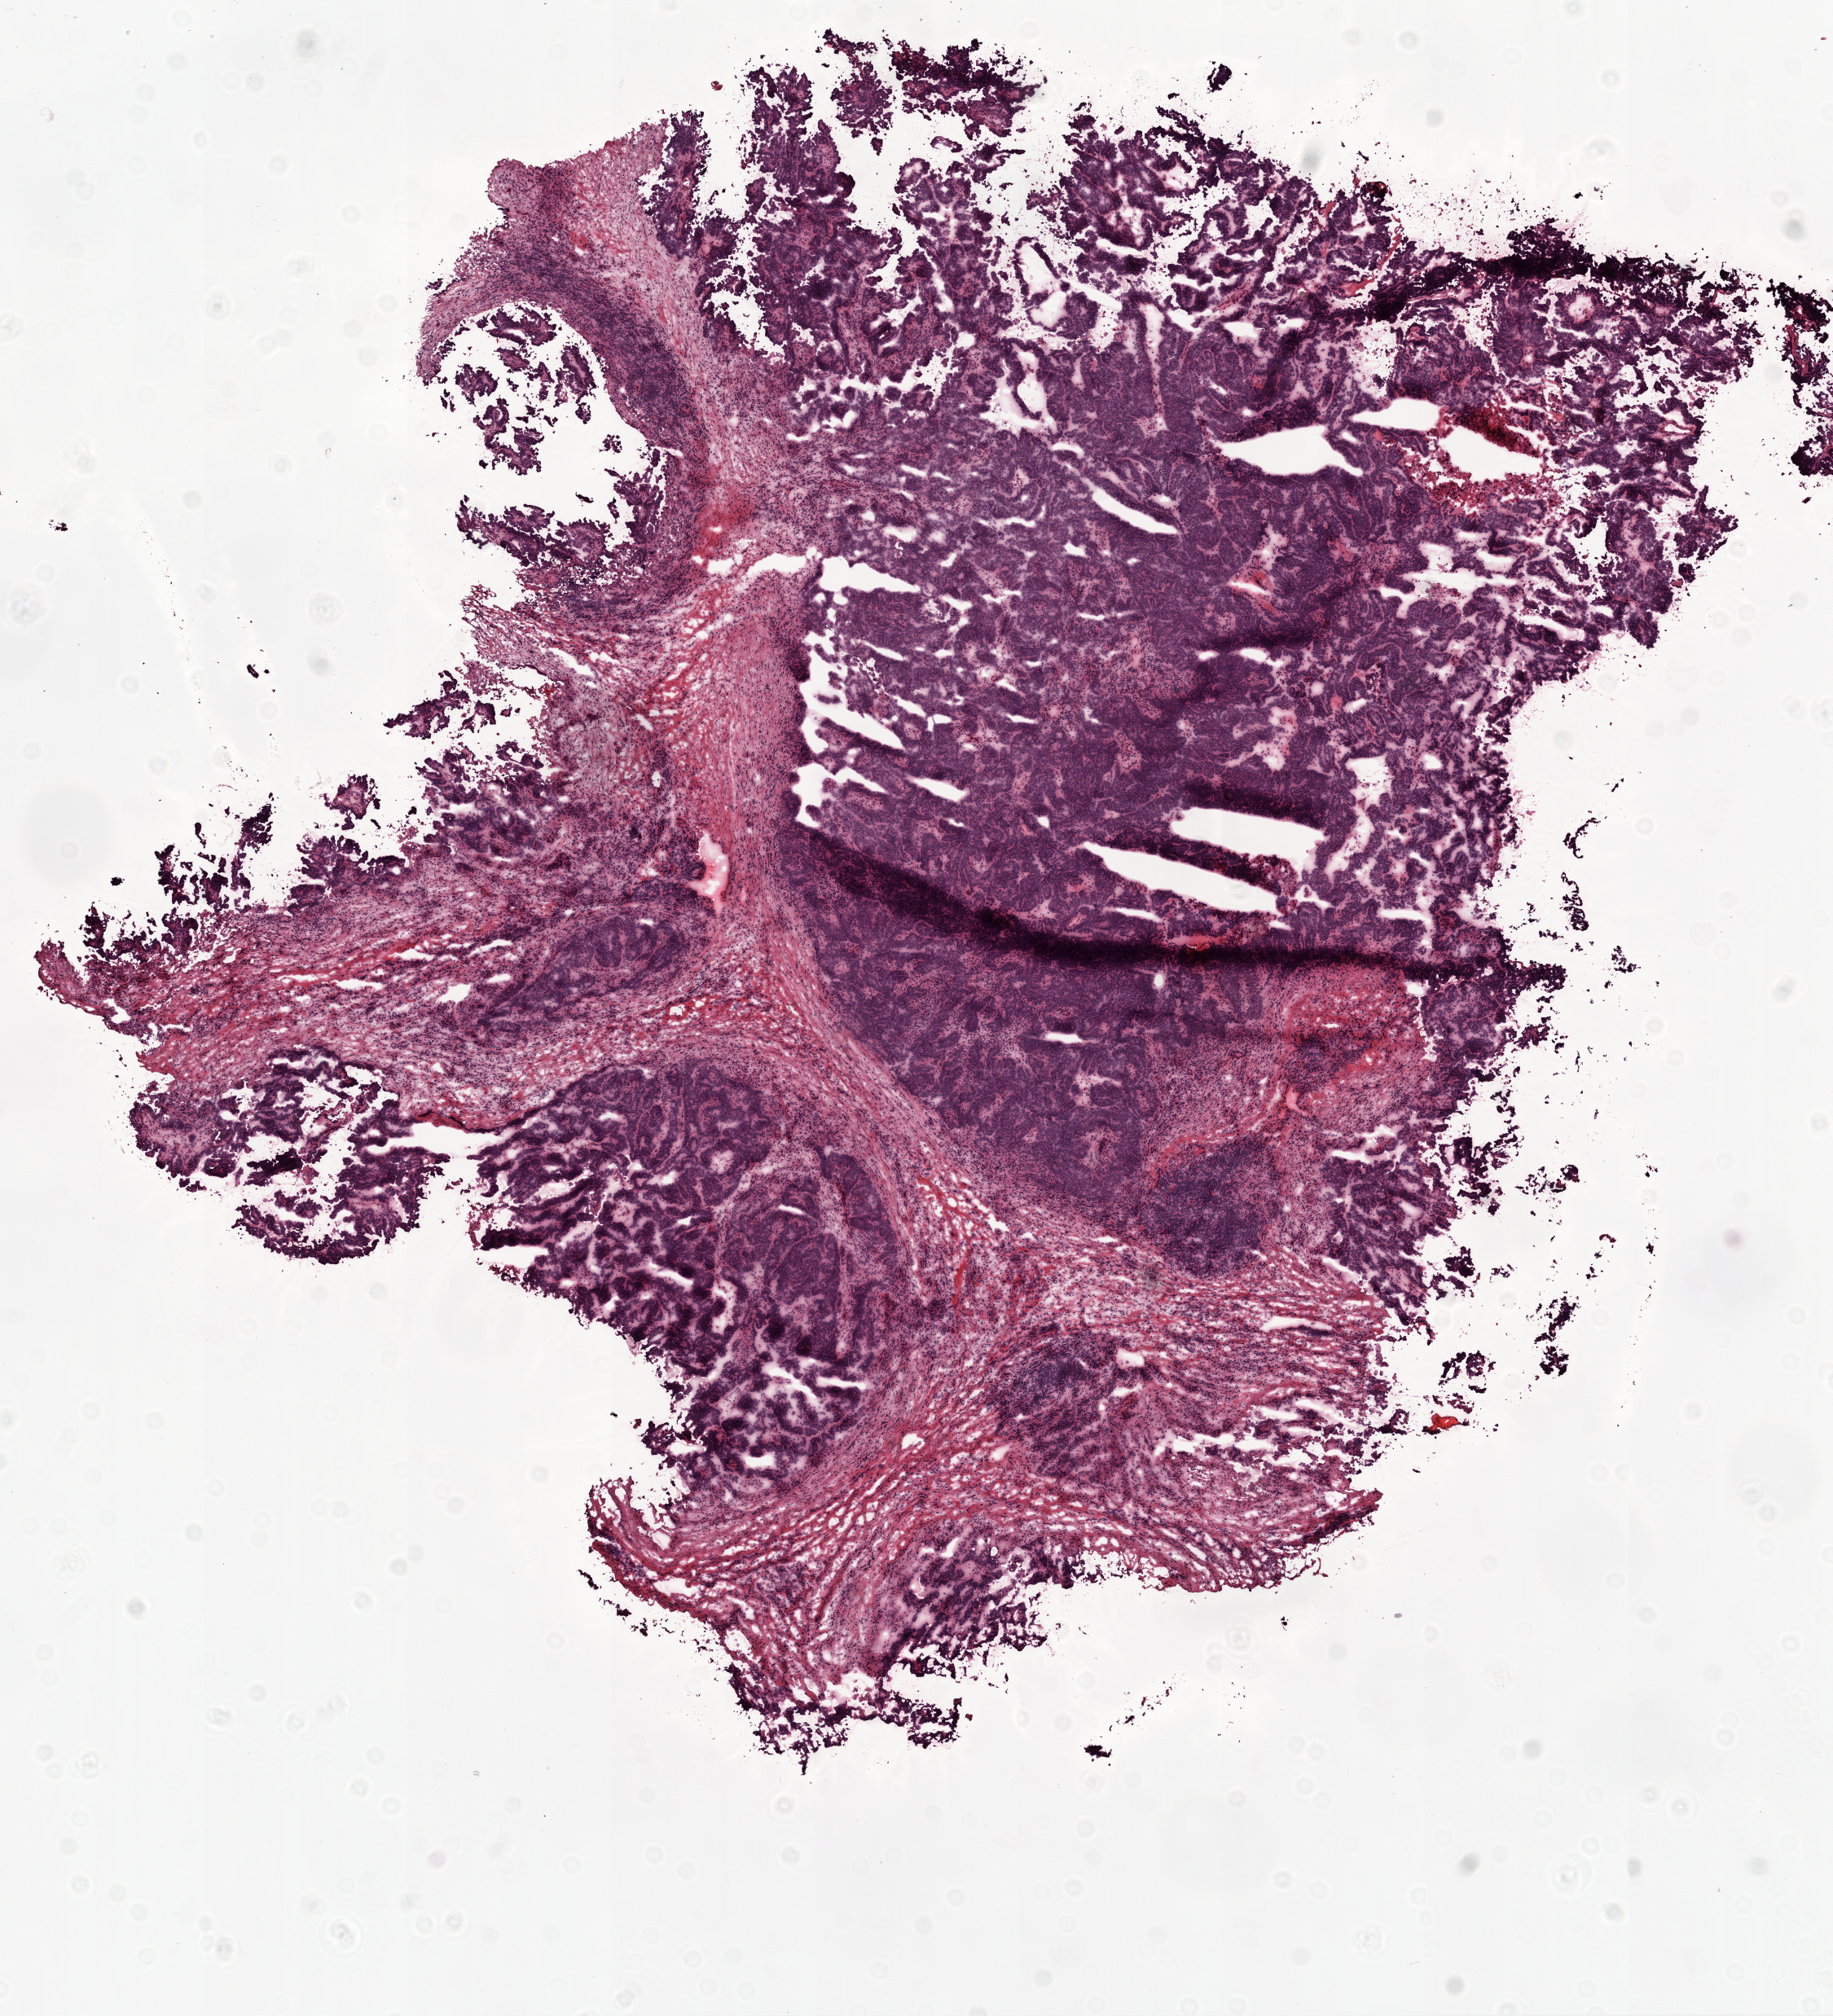
Digitized H&E-stained tissue section (whole slide) — a low-resolution overview of the entire scanned area, about 9.0 x 9.9 mm; frozen section from the top of the tissue portion; recurrent tumour sample from the ovary. Patient: female, age at initial diagnosis 75 years. Pathologist review of this section (percent, as recorded): tumour cells 60%, tumour nuclei 90%, normal cells 0%, stromal cells 30%, necrosis 10%.
This section: recurrent tumour. Patient diagnosis: Serous cystadenocarcinoma, NOS.